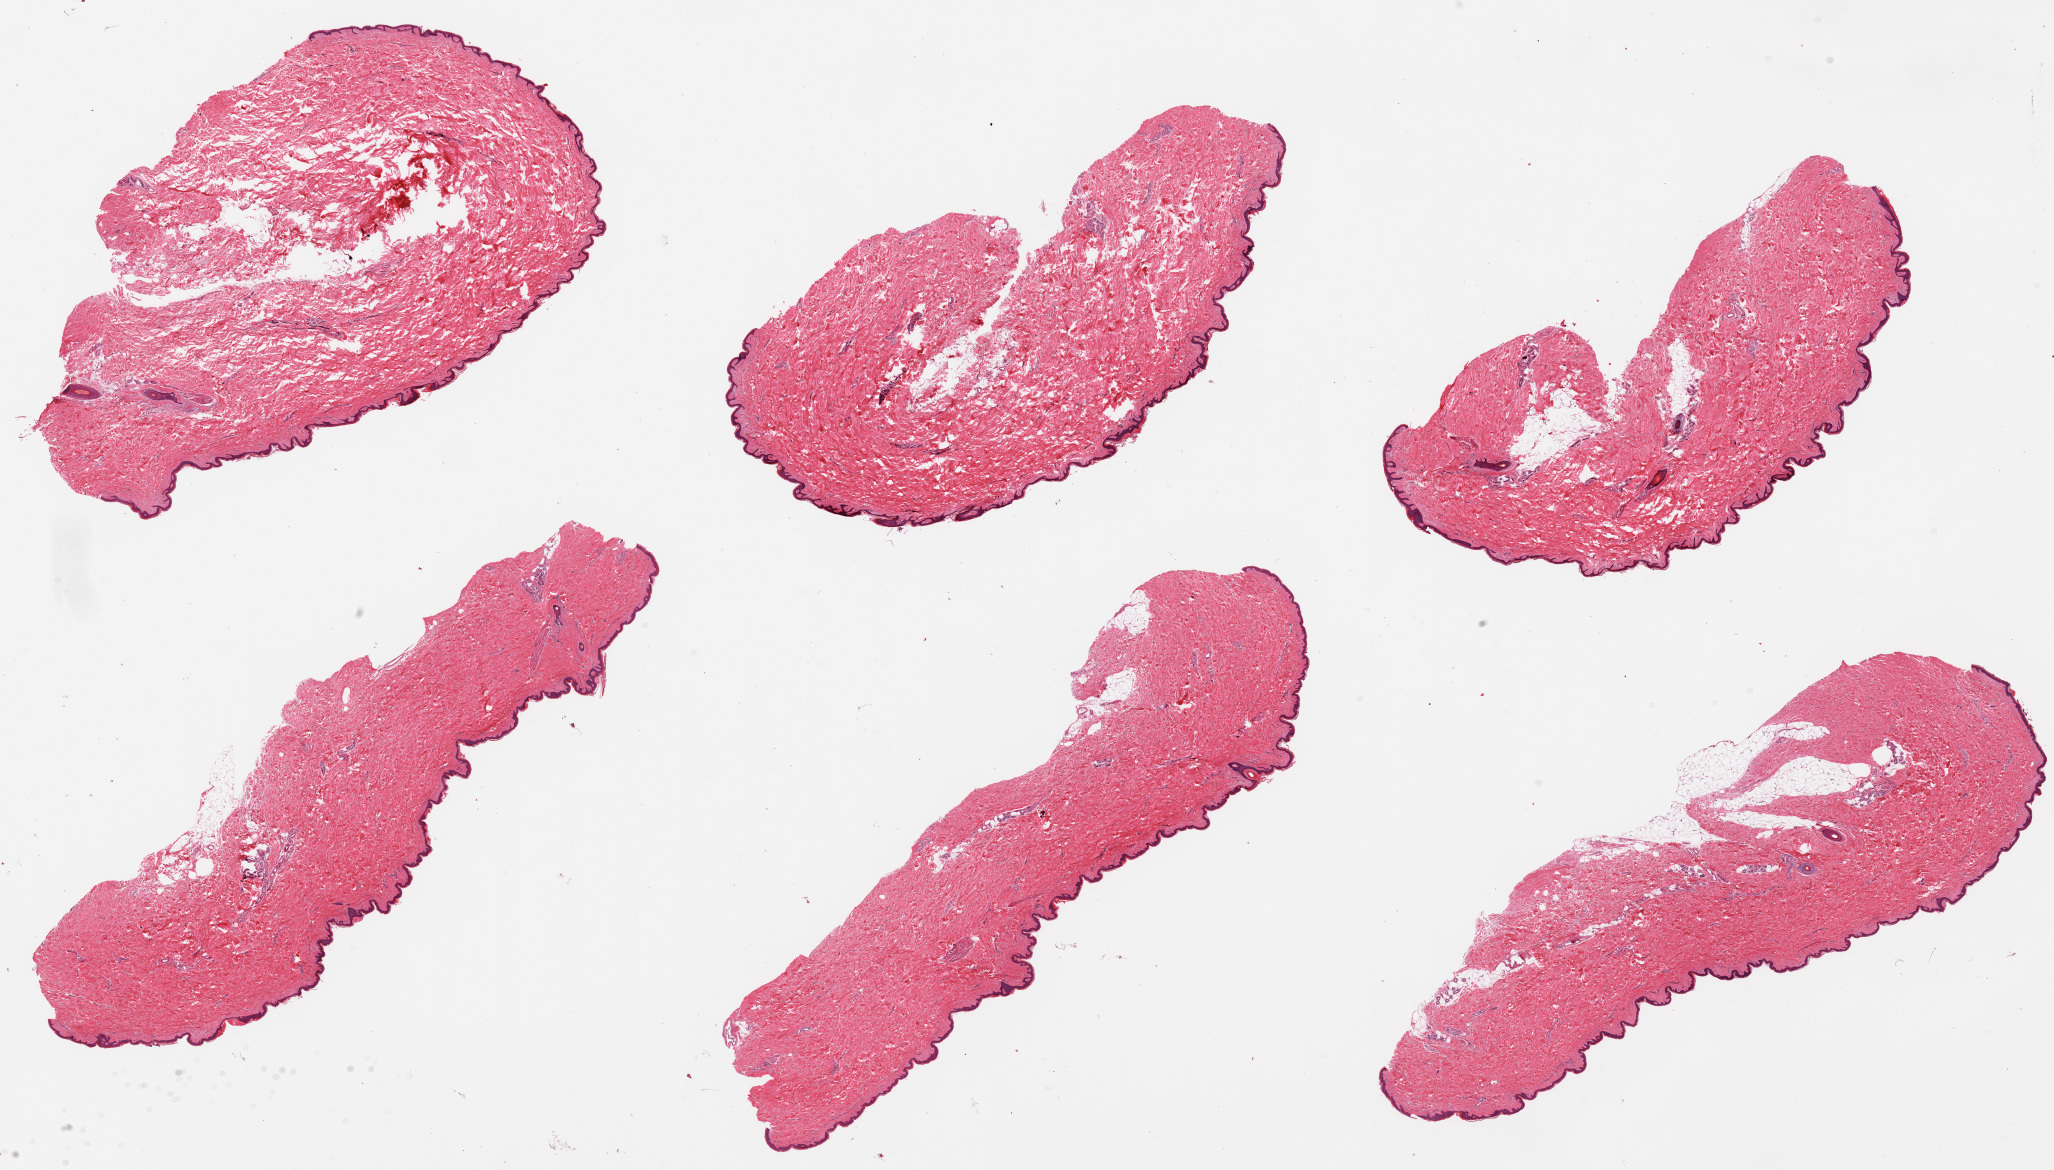
Whole-slide image, hematoxylin and eosin (H&E) stain — whole scanned area (about 32.5 x 18.5 mm) shown as a low-resolution overview, PAXgene-fixed, paraffin-embedded tissue, target tissue: skin of suprapubic region, donor tissue sample. Male donor.
Review note (as recorded): 6 pieces; well trimmed.